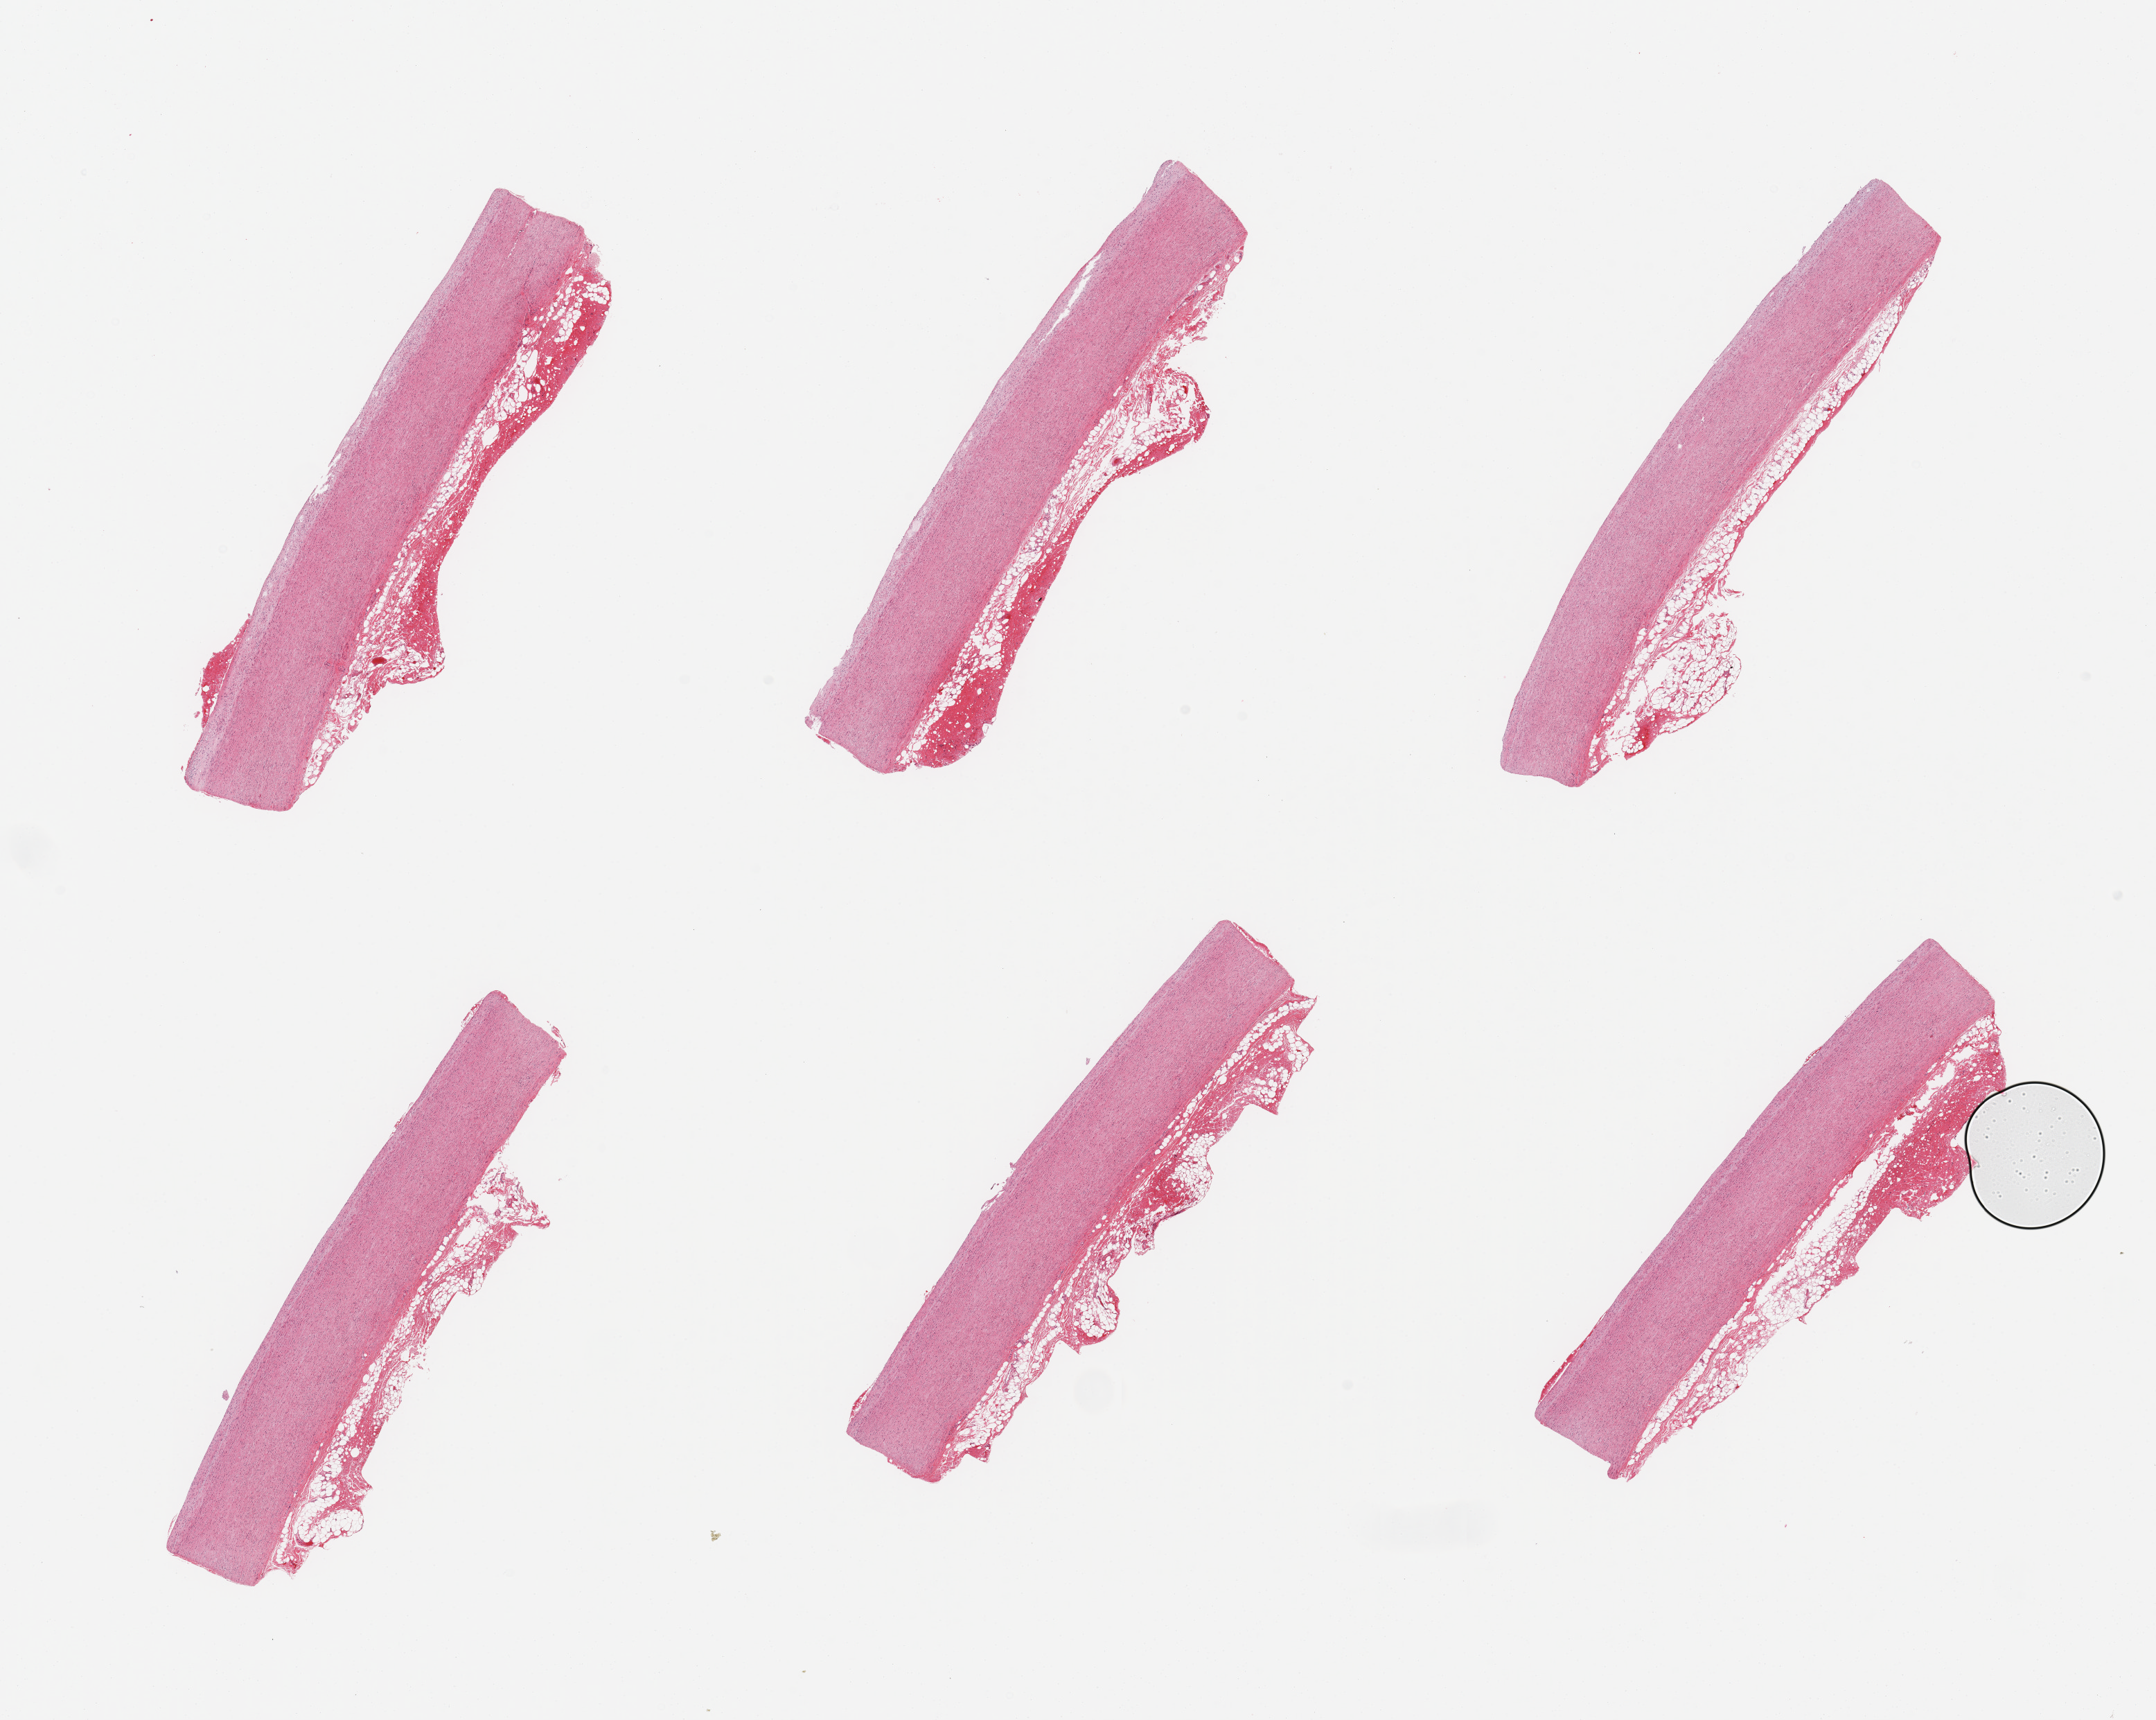
Digitized H&E-stained section — whole scanned area (about 24.6 x 19.6 mm, acquisition: 20x scan) shown as a low-resolution overview. PAXgene-fixed paraffin-embedded (PFPE) section. Sampled site (target tissue): aorta. Tissue donor sample. Donor: male.
Review note (as recorded): 6 pieces; evolving atherosclerotic plaque, attached ~1mm congested adventitia.